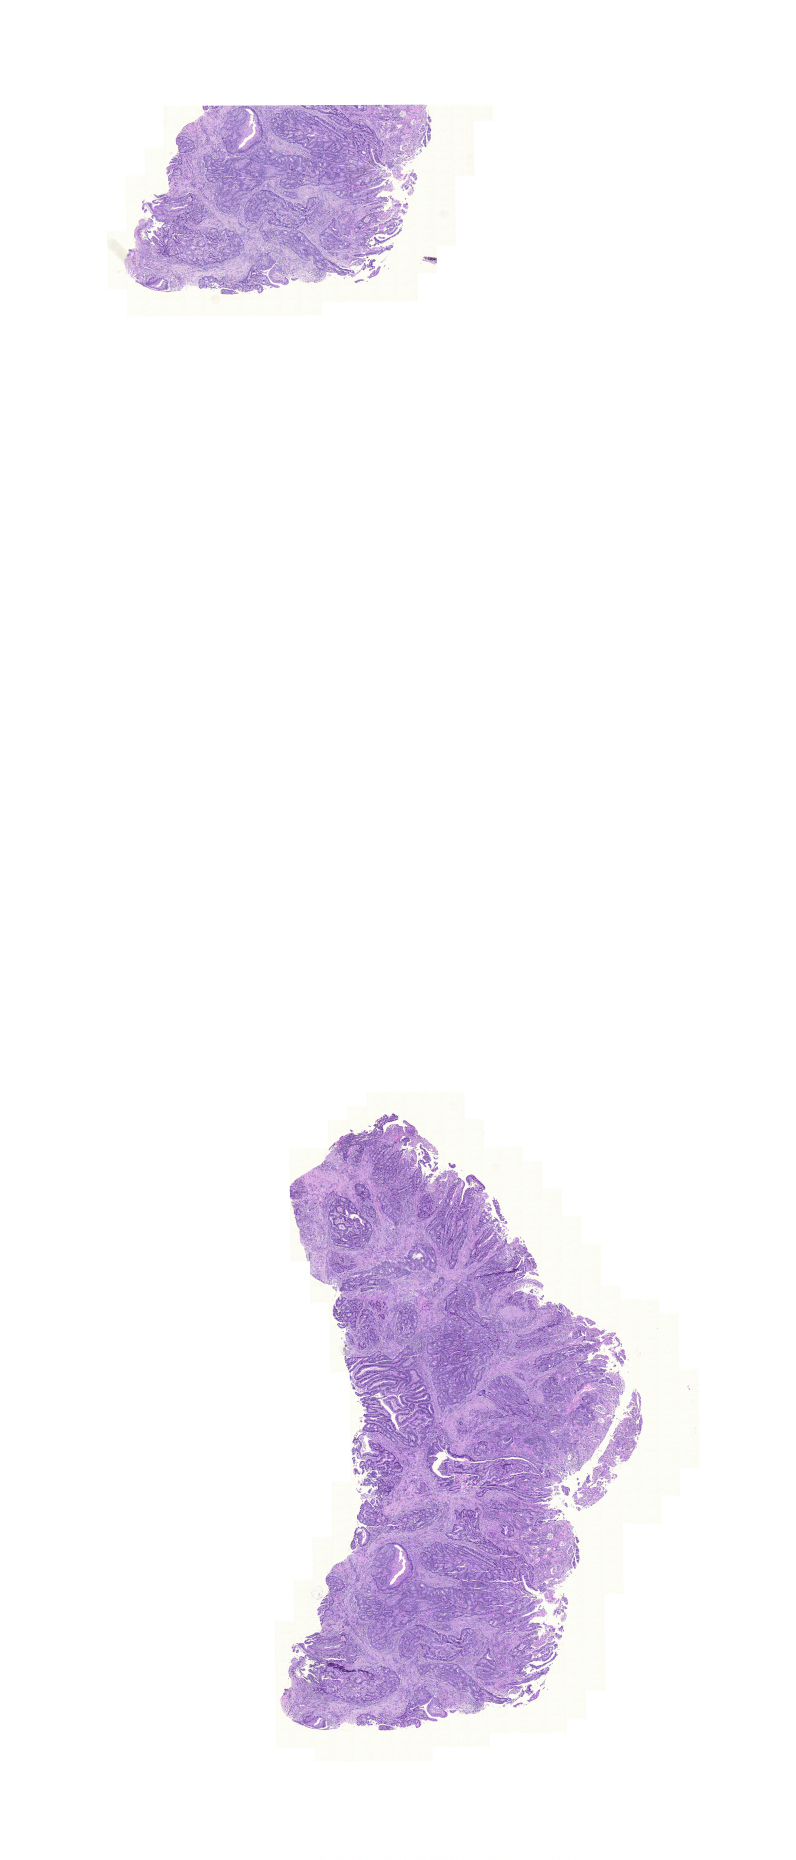
Whole-slide histology image, H&E — whole scanned area (about 11.8 x 27.7 mm) shown as a low-resolution overview, formalin-fixed paraffin-embedded (FFPE) diagnostic section, sample: primary tumour, colon. Male, age 70 years at initial diagnosis.
* AJCC pathologic stage: I
* pathologic diagnosis: Adenocarcinoma, NOS (ascending colon)
* lymph nodes positive (case pathology): 0 of 28 examined